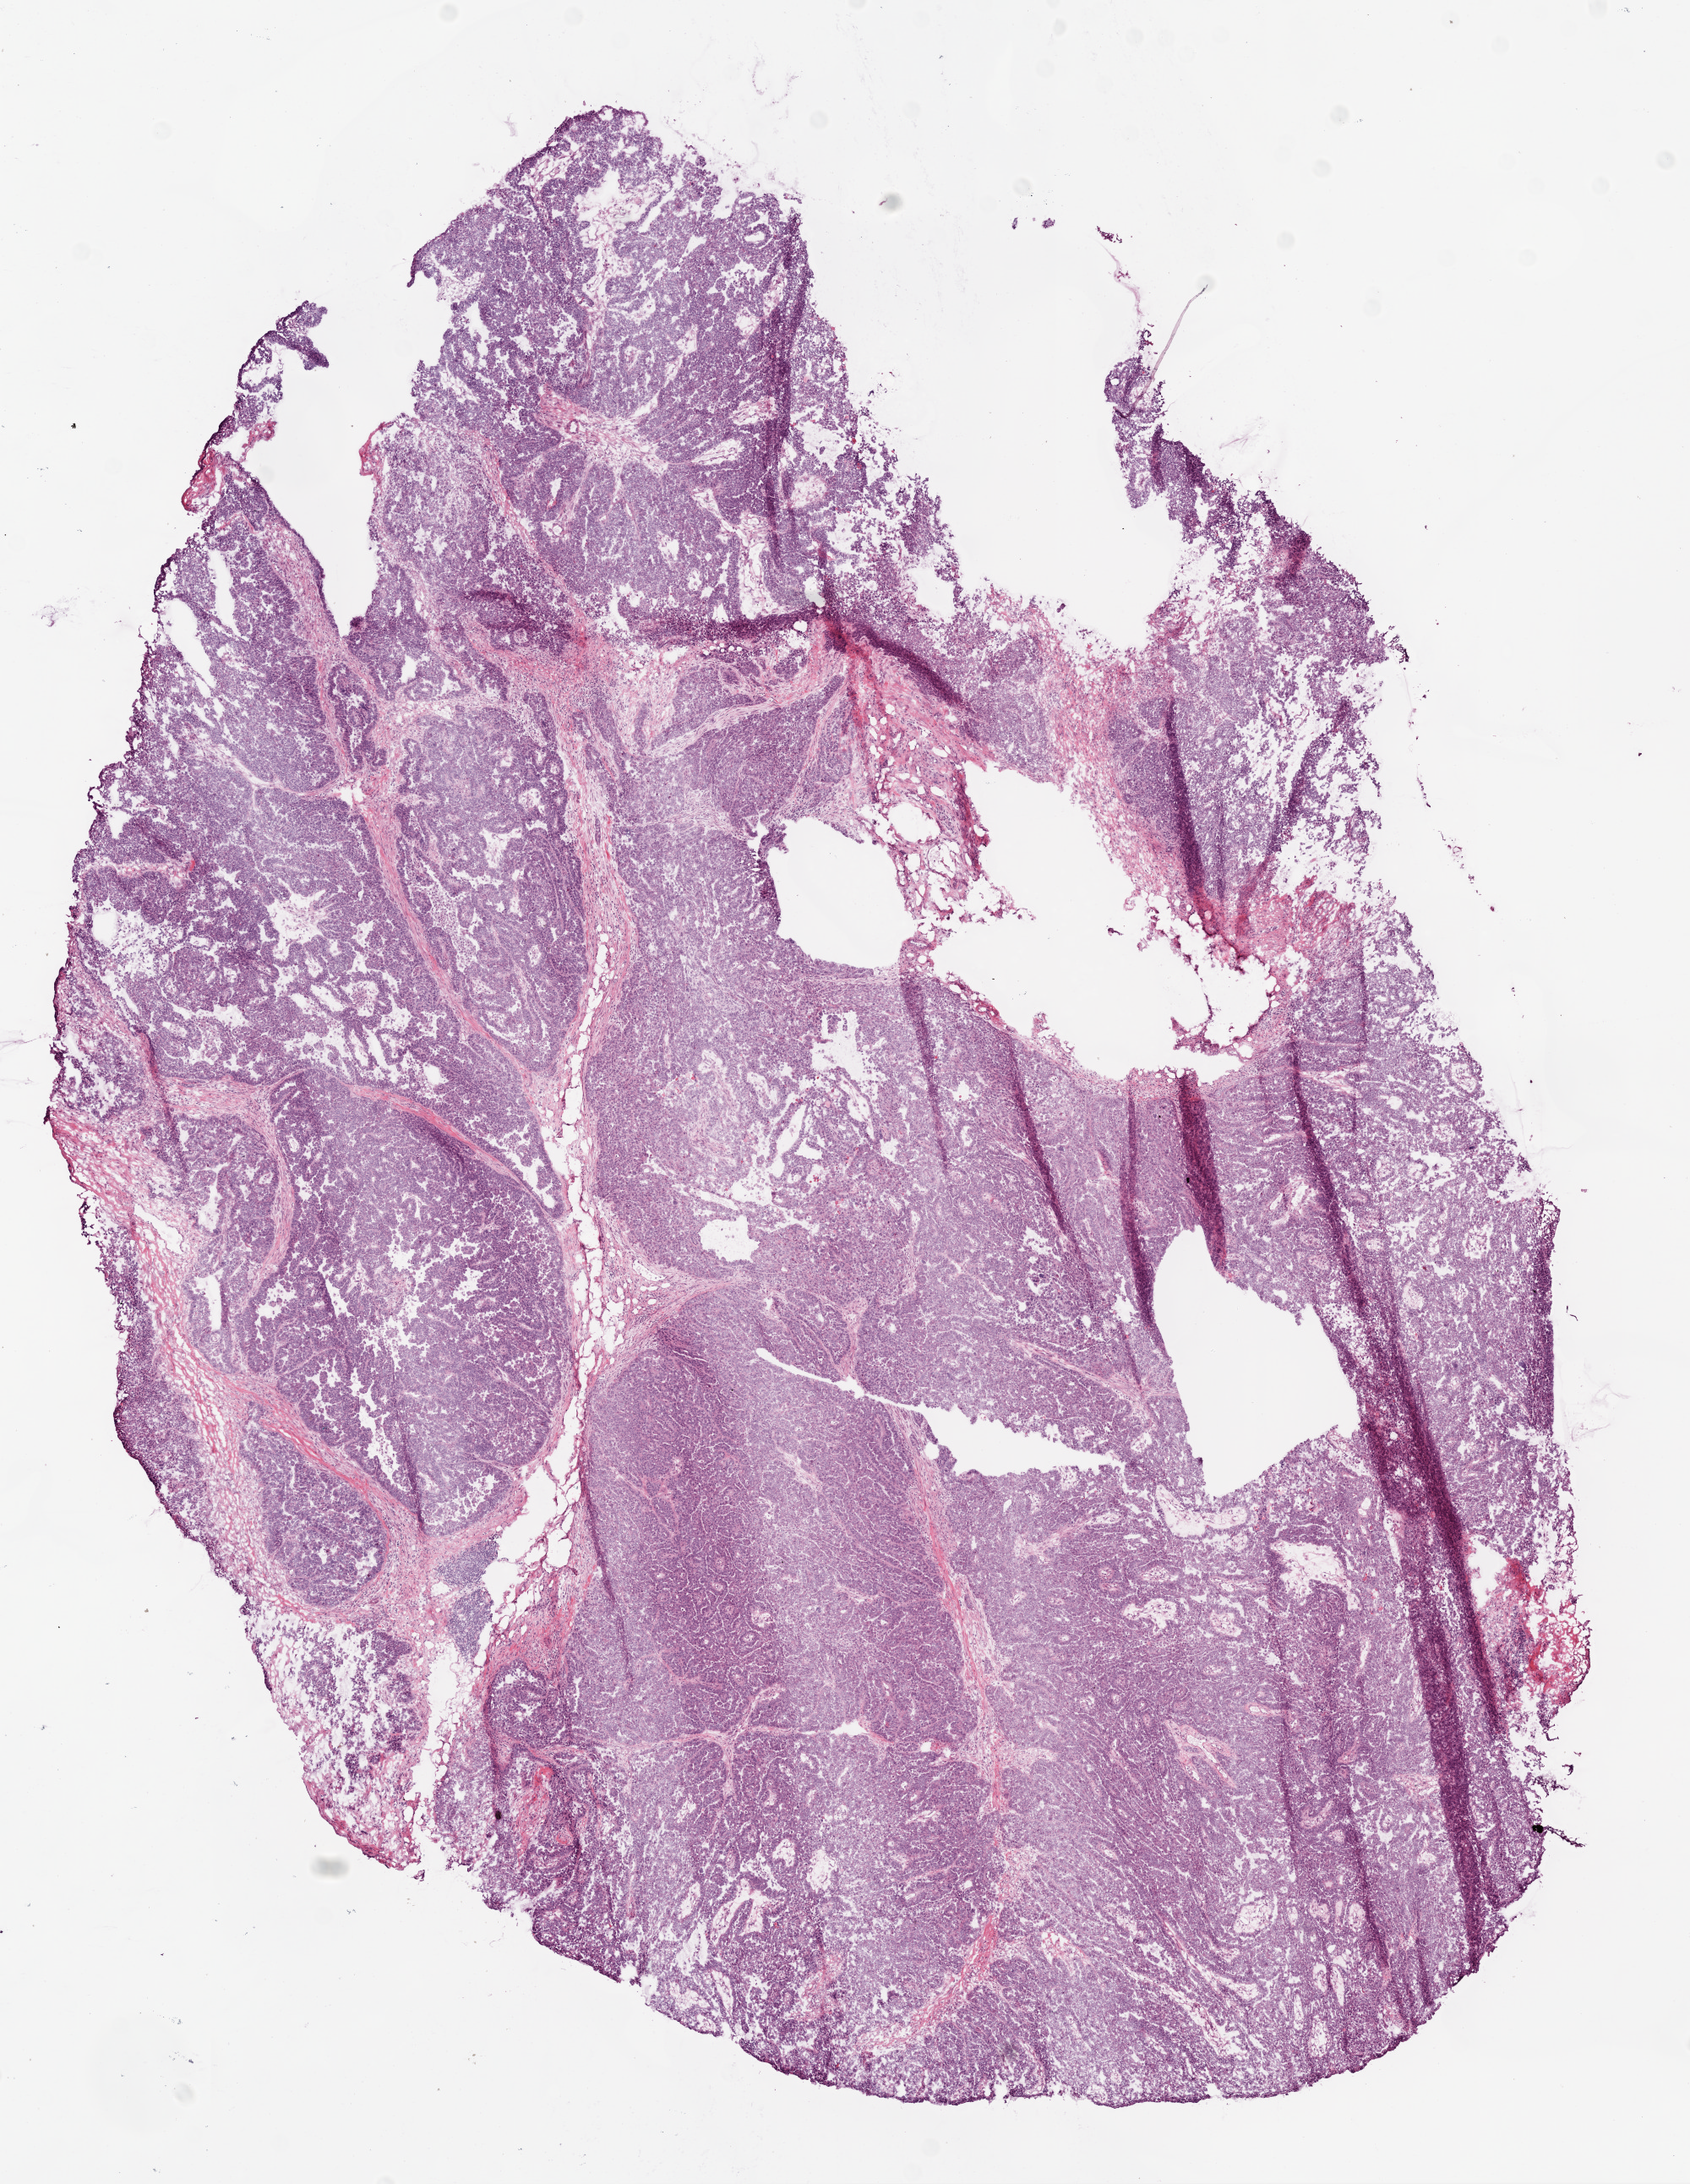
H&E whole-slide image, shown as a low-resolution overview of the whole scanned area (about 8.0 x 10.4 mm, slide scanned at 20x); frozen section; ovary, primary tumour sample. Patient: female, age at initial diagnosis 51 years. Composition of this section per pathologist review: tumour cells 98%, tumour nuclei 95%.
Pathologic diagnosis: Serous cystadenocarcinoma, NOS.